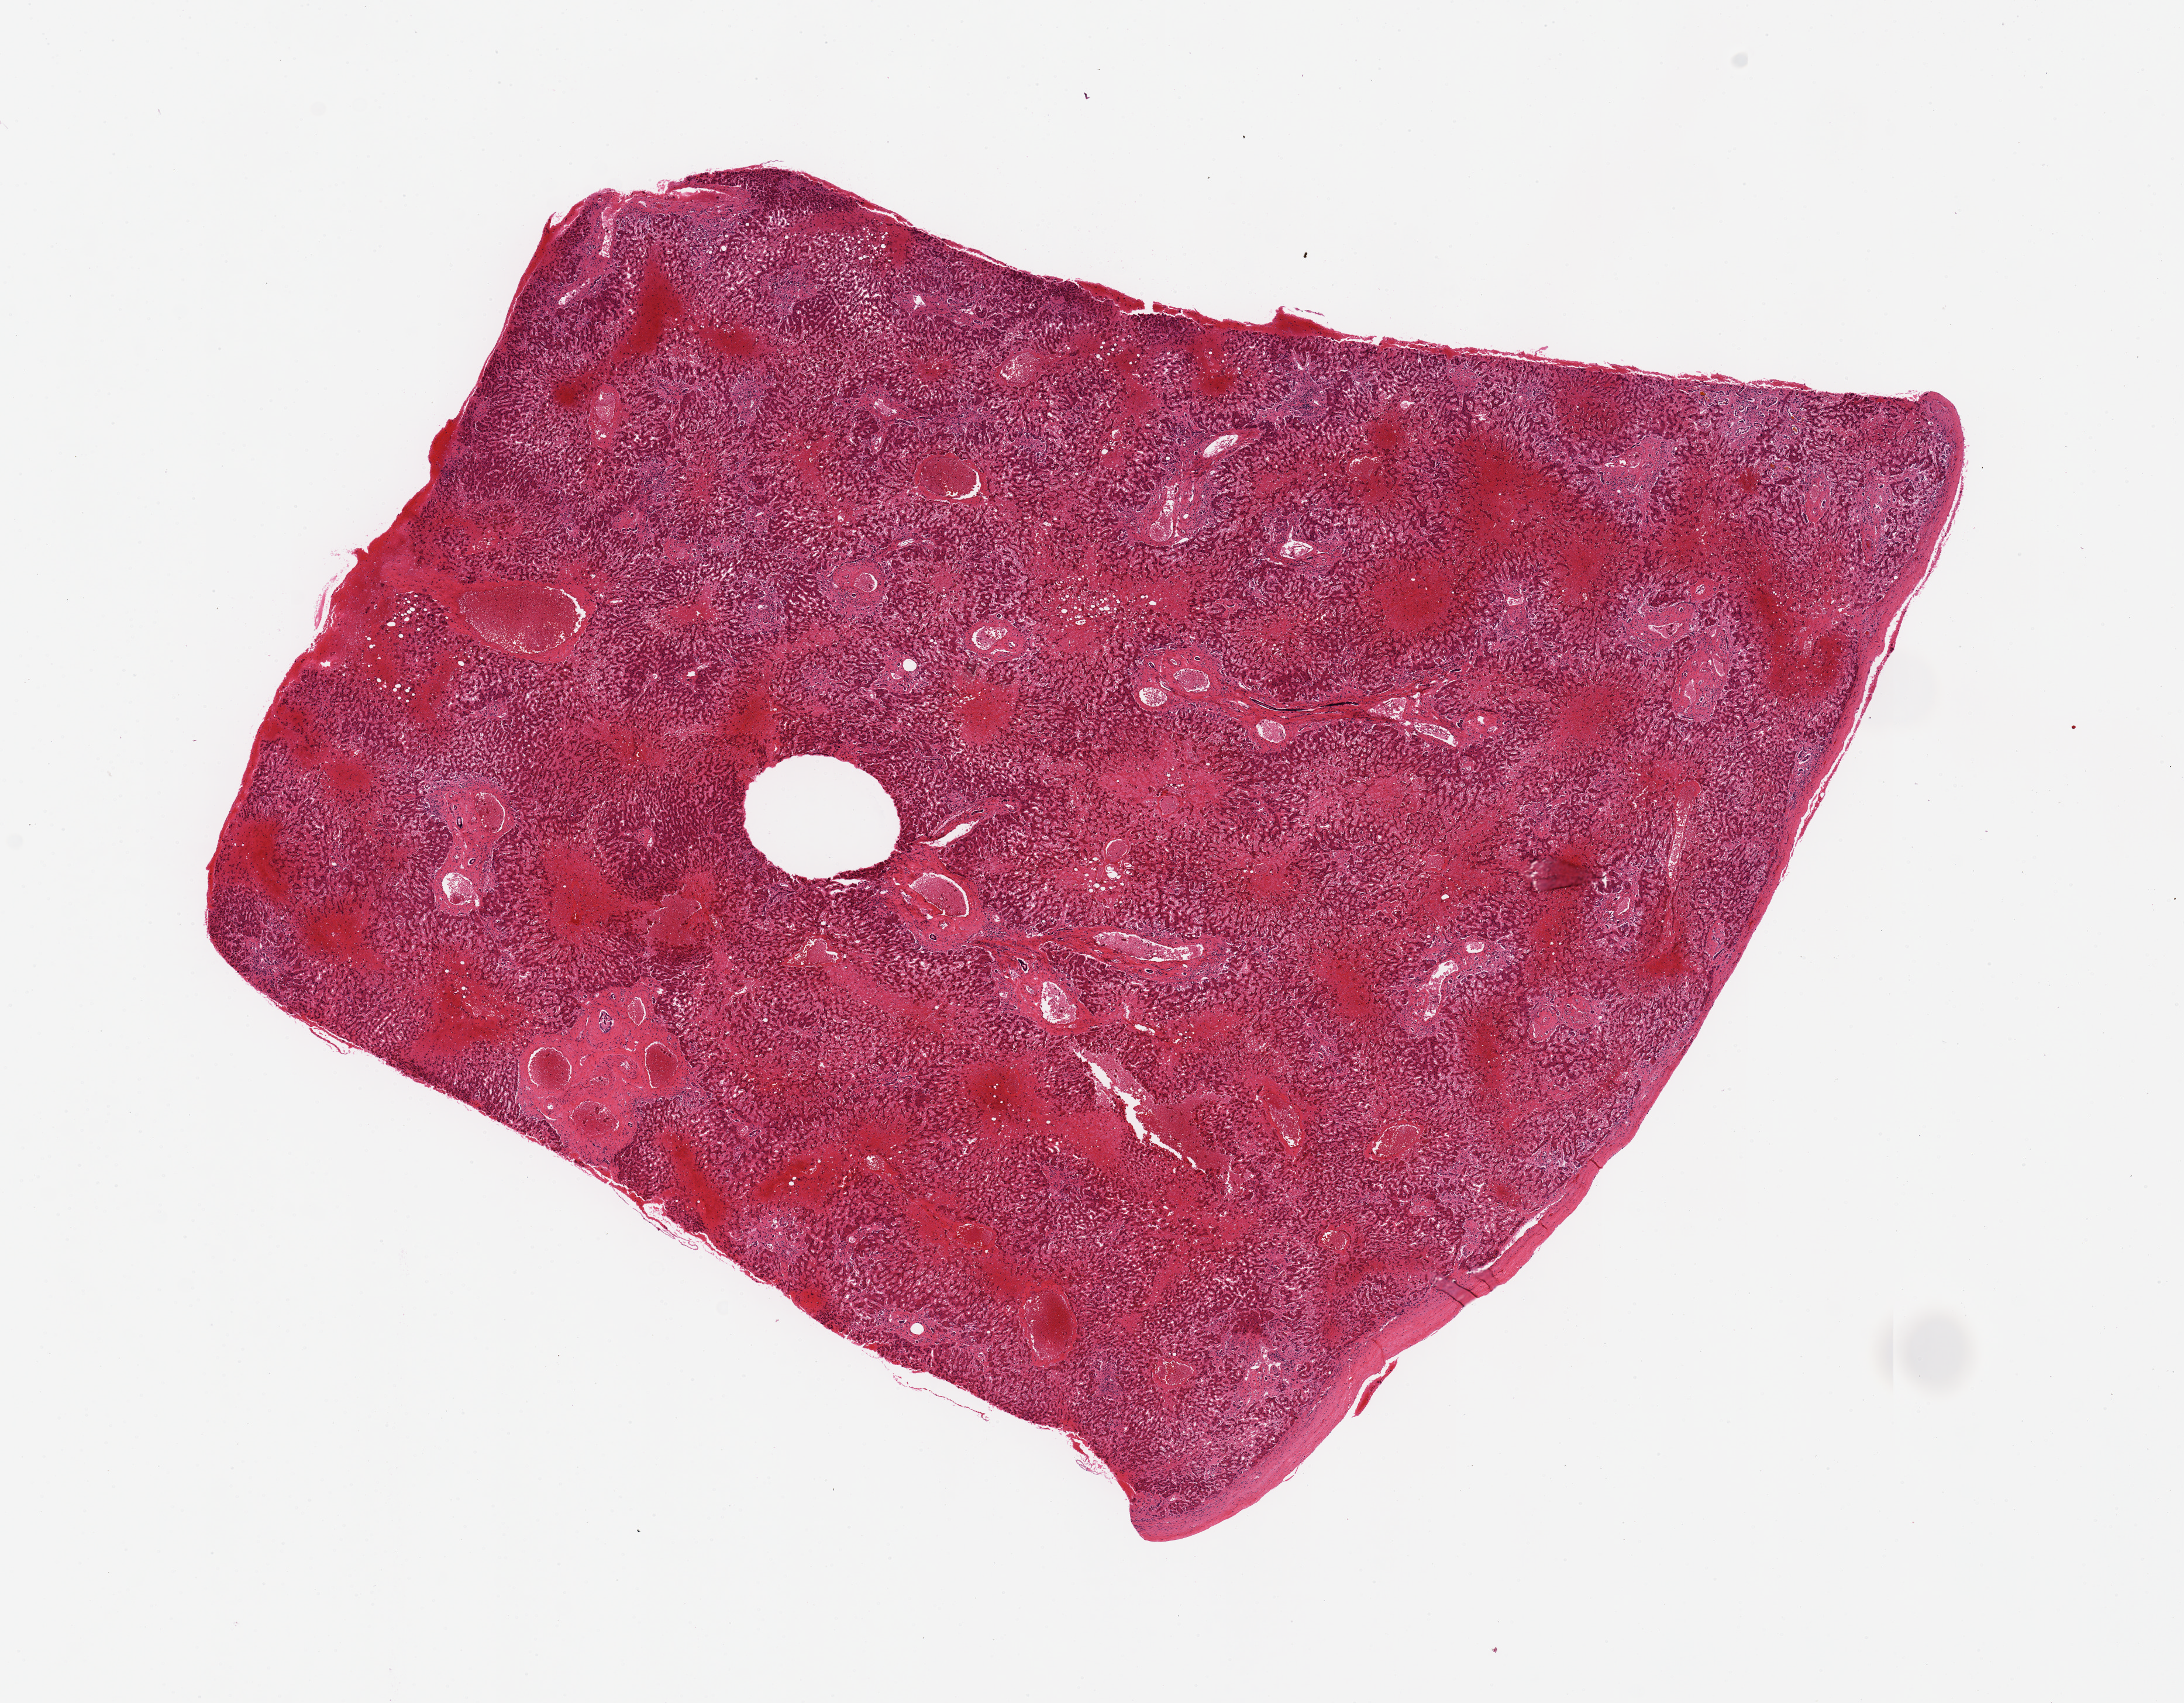
Whole-slide image, H&E stain, low-resolution overview of the scanned area, about 14.8 x 11.5 mm (slide scanned at 20x); PAXgene-fixed, paraffin-embedded tissue; sampled site (target tissue): liver; tissue donor sample. Male donor.
- review note (as recorded): 9x8 mm. Severe acute passive congestion with central necrosis